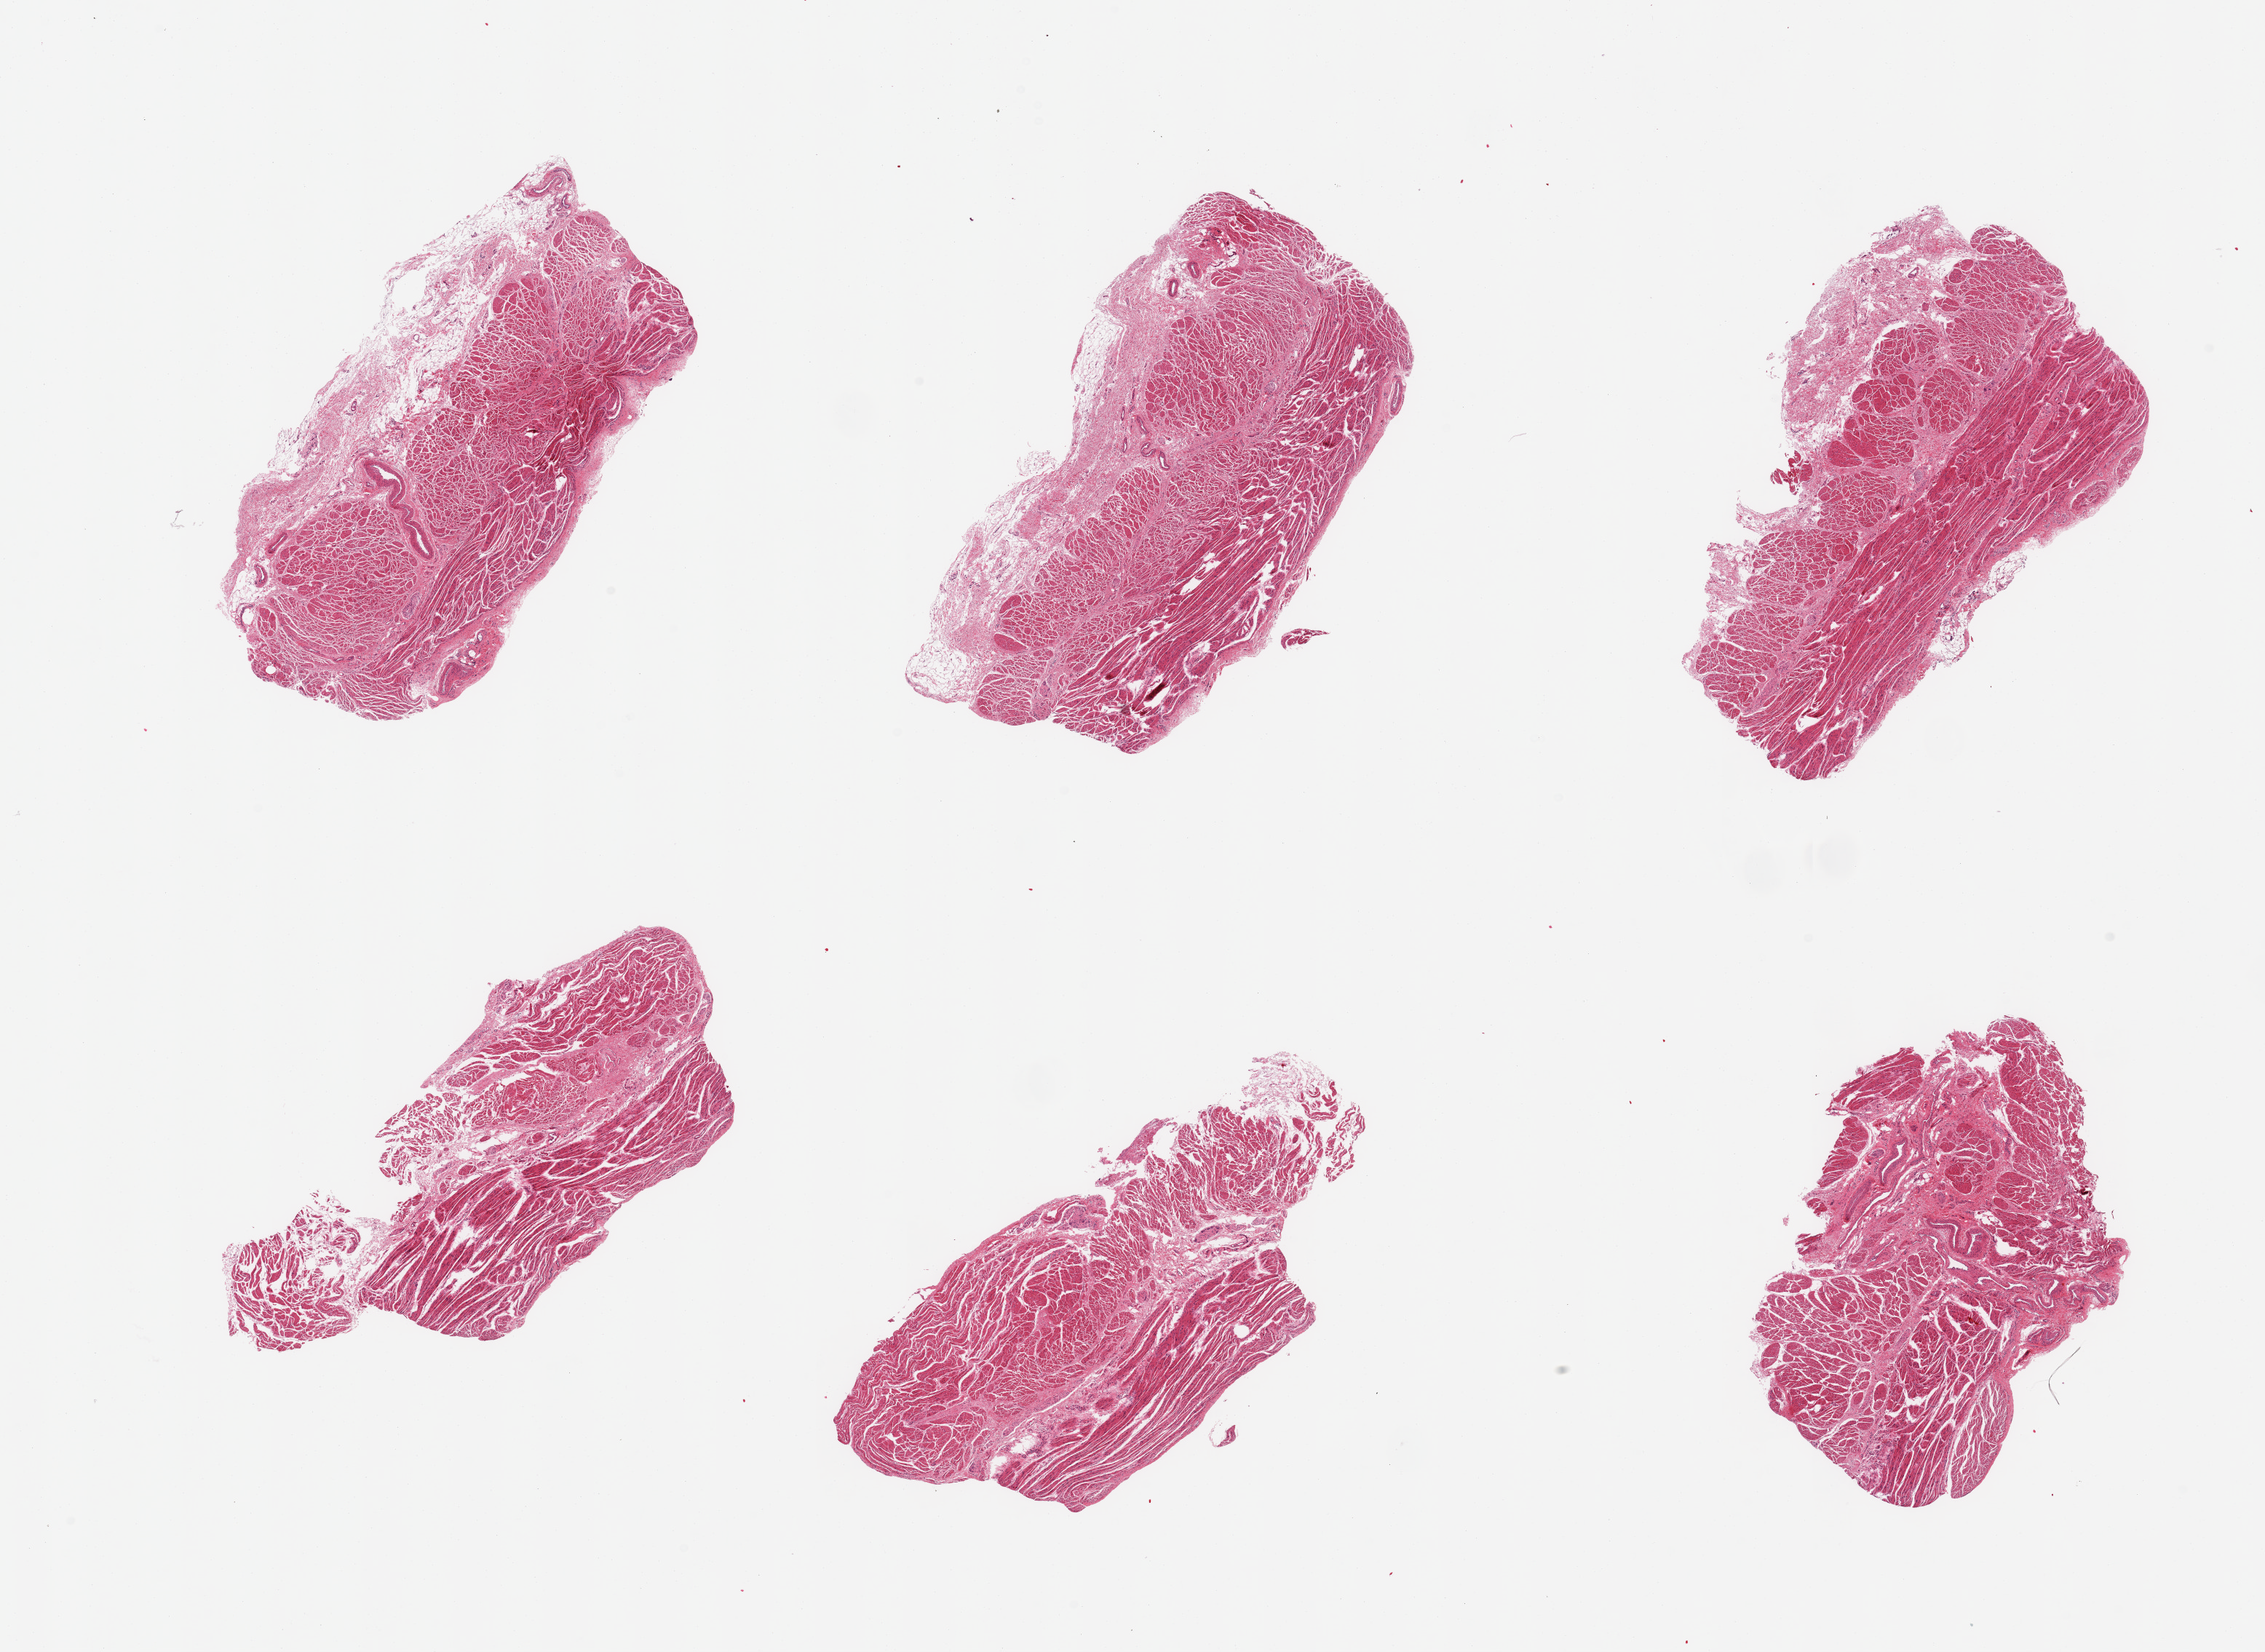
Haematoxylin and eosin whole-slide image, brightfield, low-resolution overview of the scanned area, about 24.6 x 18.0 mm. PAXgene-fixed, paraffin-embedded tissue. Sampled site (target tissue): gastroesophageal junction. Donor tissue sample. Donor sex: male.
• reviewer comment on this tissue sample: 6 pieces; target muscularis; 3 of 6 pieces with attached adventitia